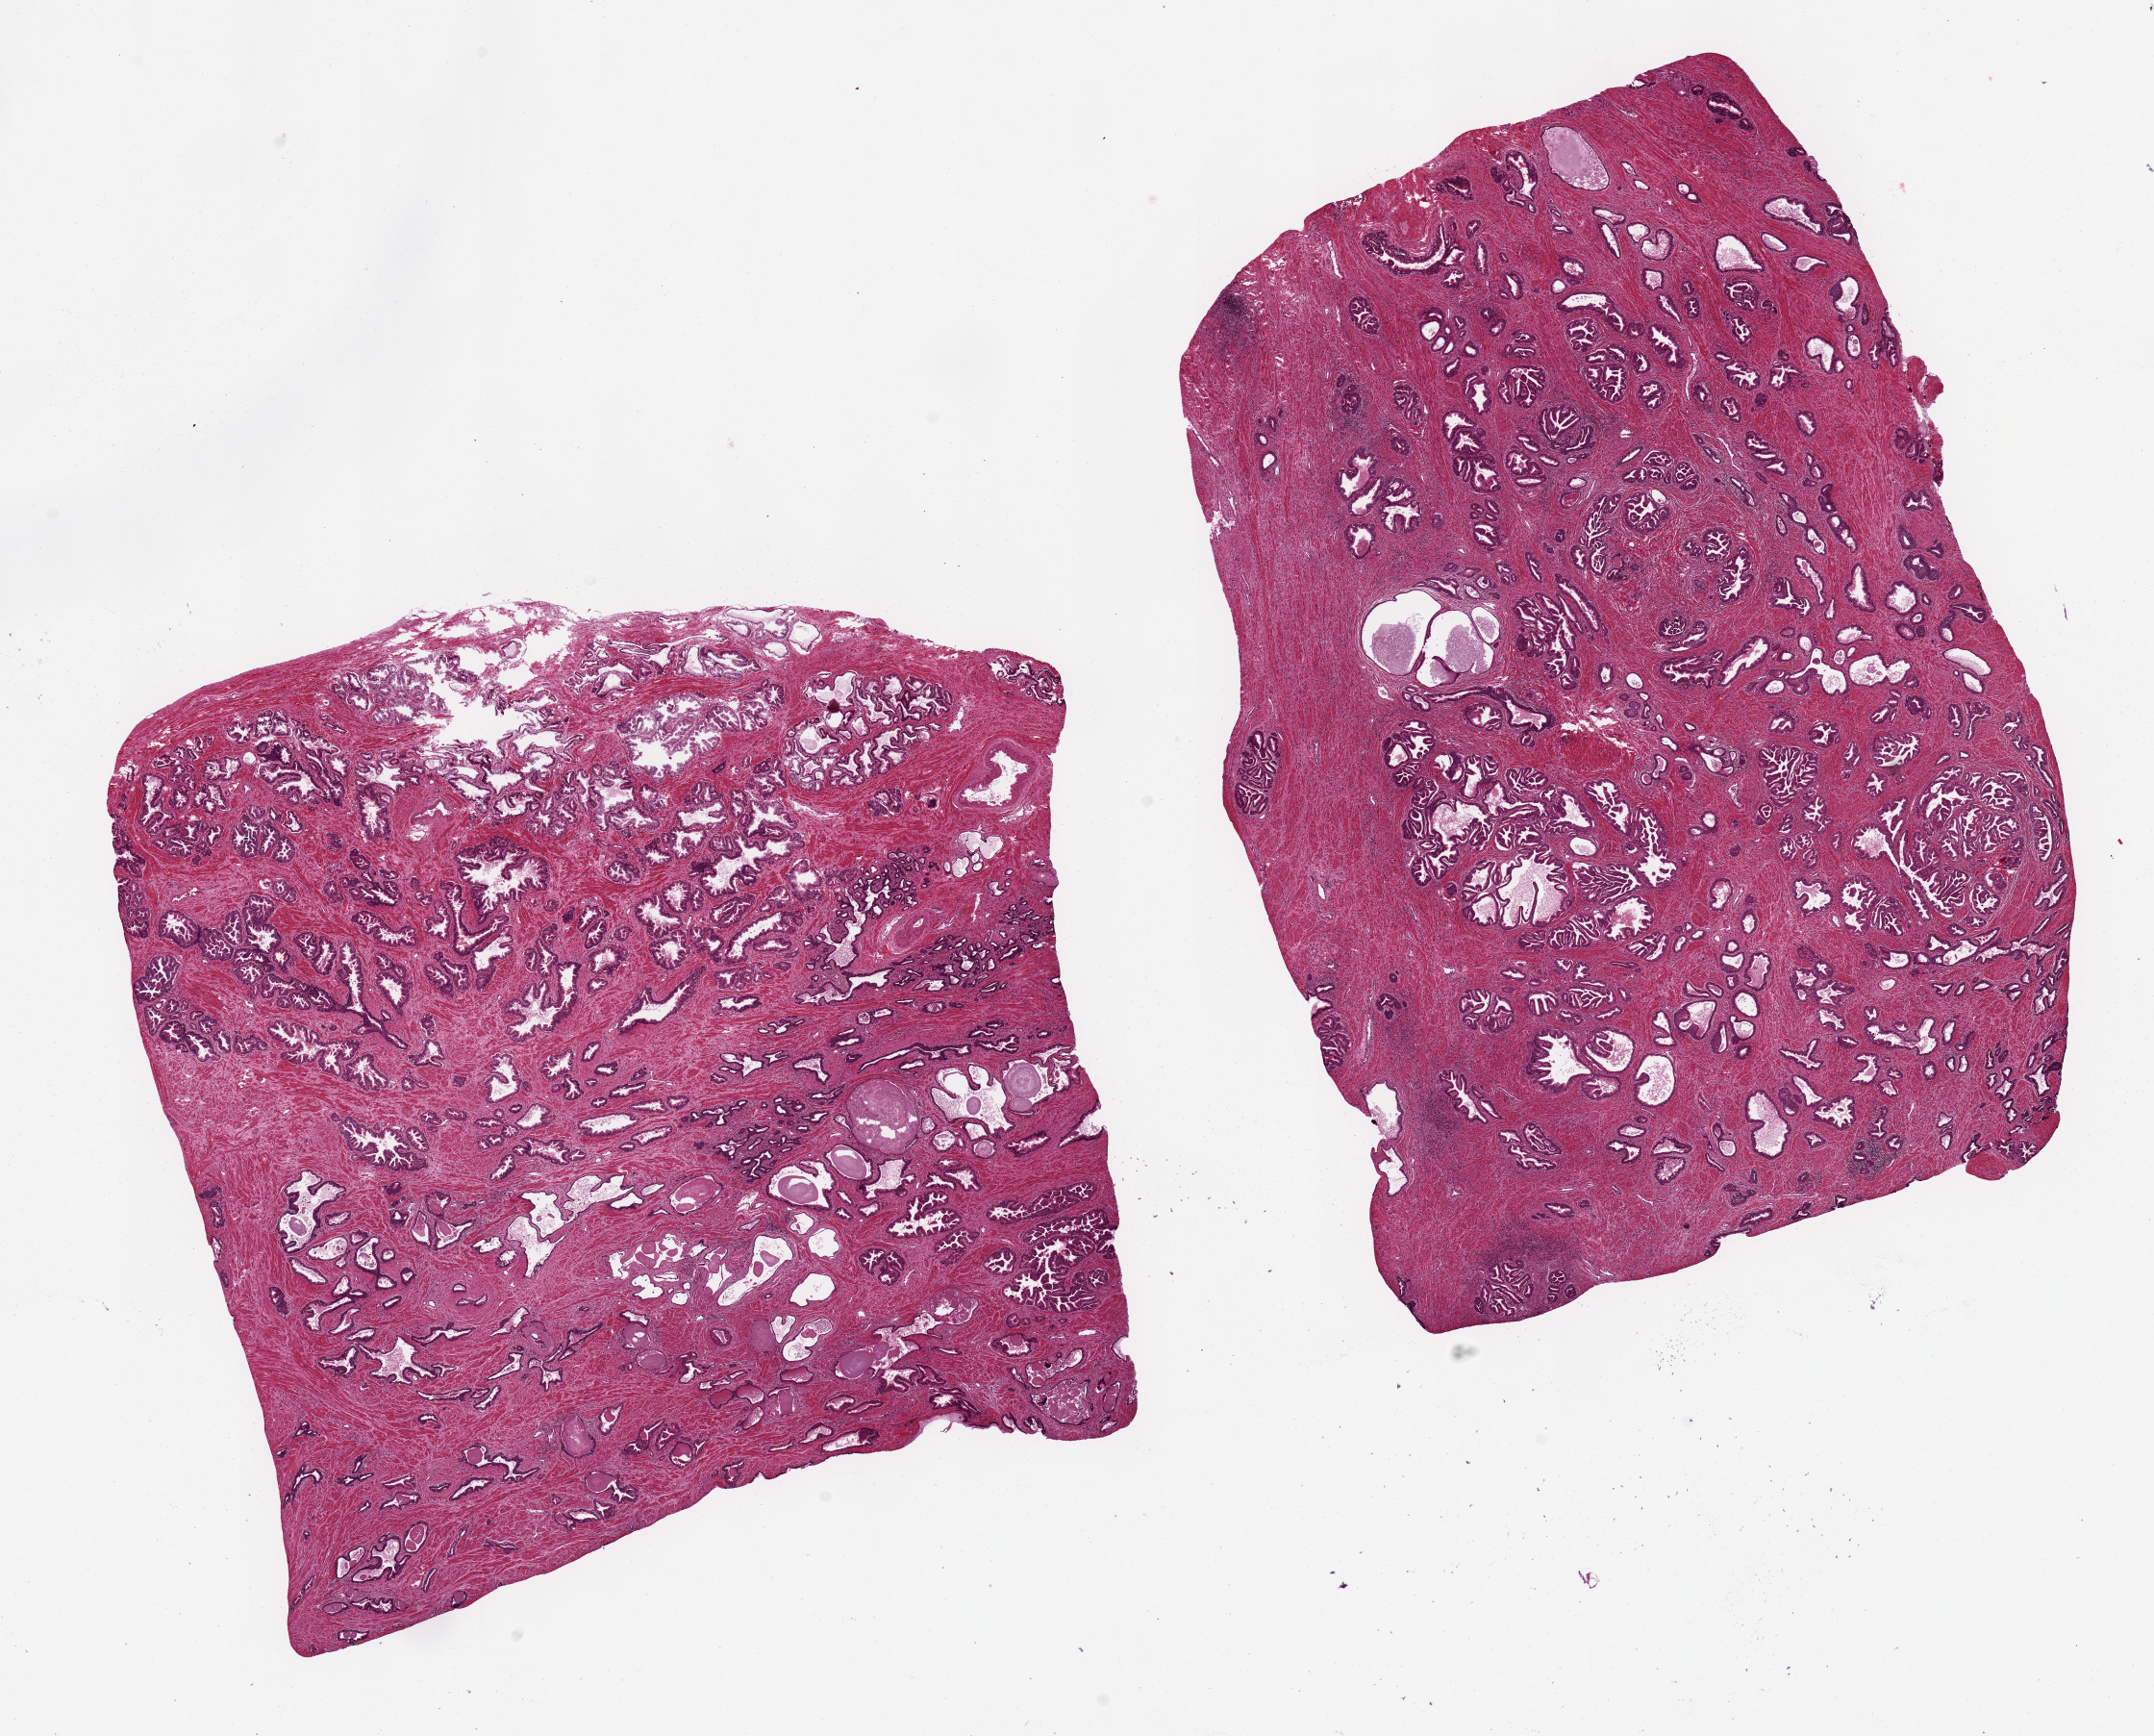
Digitized H&E-stained section — whole scanned area (about 17.7 x 14.3 mm, slide scanned at 20x) shown as a low-resolution overview; PAXgene-fixed paraffin-embedded (PFPE) section; section of prostate (target tissue); tissue donor sample. Male donor.
Review note (as recorded): 2 pieces 9x6 & 7x7 mm; hyperplastic.